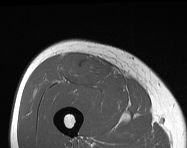
MRI of an extremity soft-tissue mass, one axial slice. MR volume resampled by the dataset authors to the PET/CT grid (not the native acquisition matrix). 3.27 mm slice thickness. 187 × 148 image matrix. Male patient. From the clinical record (not read from this slice): histological type: pleiomorphic leiomyosarcoma; grade: intermediate; site of the primary tumour: right thigh.
Outlined on this slice (expert contour drawn on MRI and transferred to this co-registered scan by the dataset authors):
- gross tumour volume including surrounding oedema: bounding box <61,54,110,87> (left, top, right, bottom; pixels)